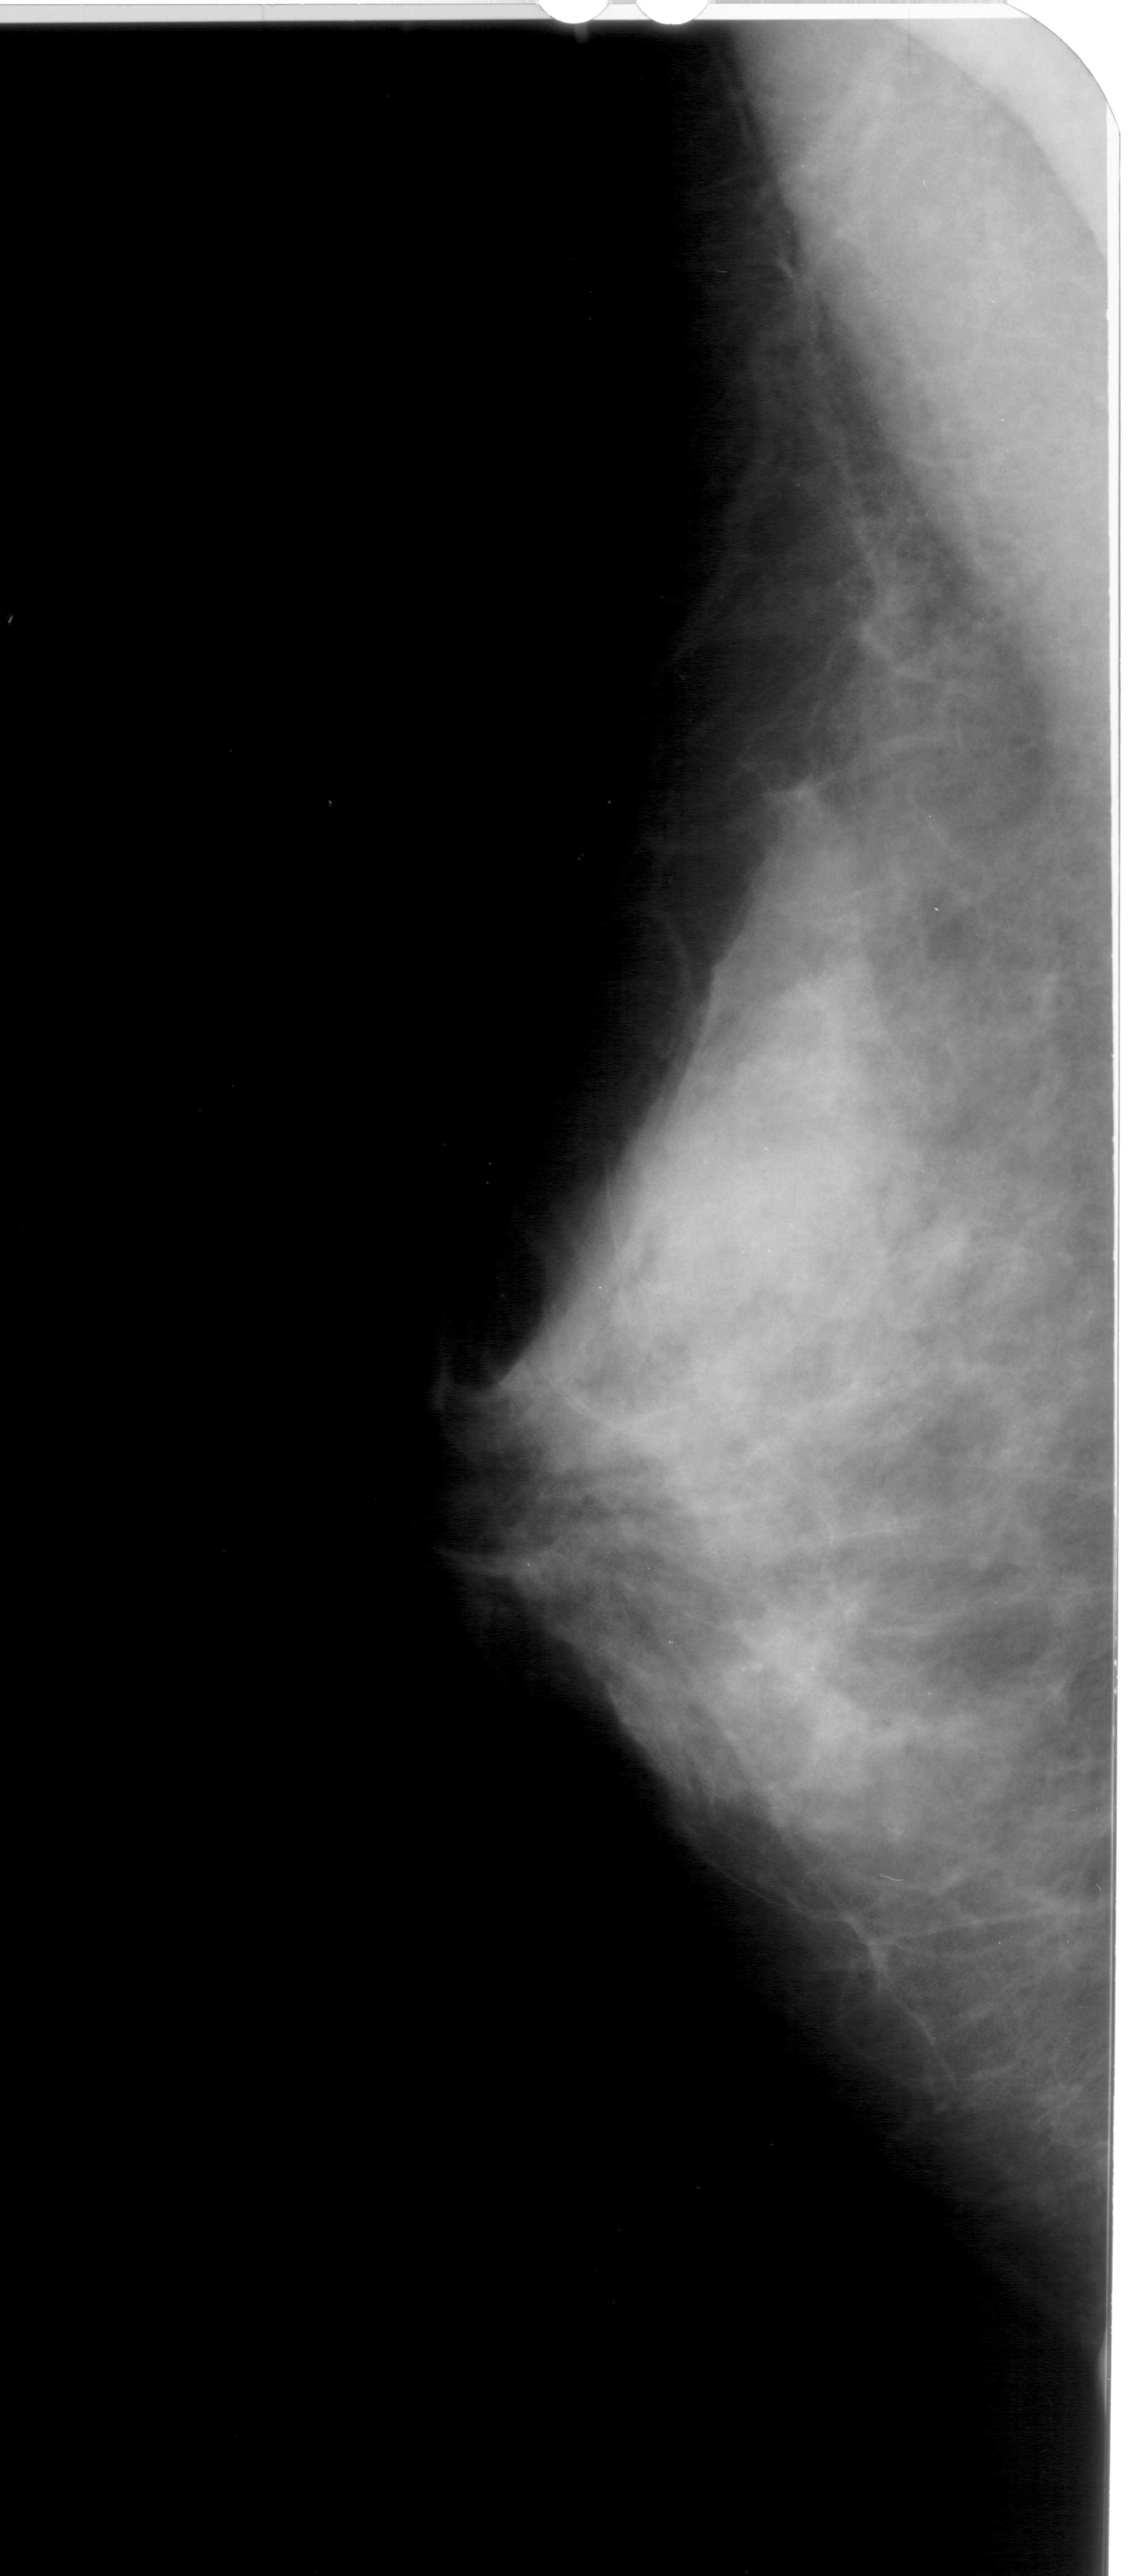
Mammogram (digitized film). Left breast. MLO view. BI-RADS breast density category 4 (scale 1–4). 1130 × 2576 image matrix.
Expert-marked regions of interest on this image (one box per marked abnormality):
- calcifications, morphology amorphous, distribution clustered; BI-RADS assessment category 4; subtlety rating 3 on a 1 (subtle) to 5 (obvious) scale; pathology (as recorded): benign: bounding box (x1, y1, x2, y2) in pixels: (641, 1548, 895, 1824)